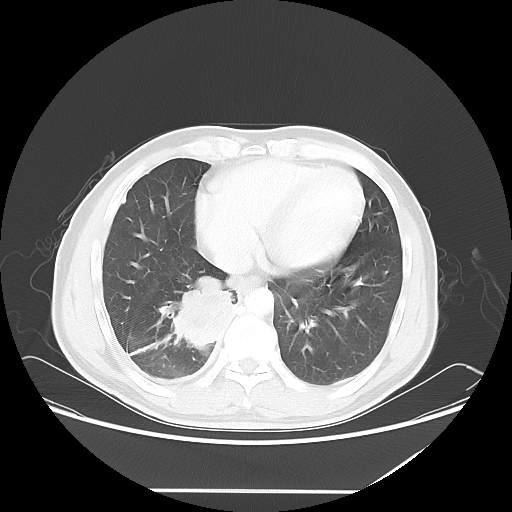
Chest CT, one axial slice; slice 21 of 60 in the series (ordered by position); reconstruction kernel LUNG; lung window (W 1500 / L -600 HU); 512 × 512 image matrix, field of view 419 × 419 mm. Patient: male, 48 years. From the clinical record (not read from this slice): clinical TNM (as recorded): T3 N3 M1a.
Annotated regions visible in this slice (bounding box drawn by a radiologist):
- lung tumour (recorded histology: squamous cell carcinoma): bounding box [x1, y1, x2, y2] px = [169, 275, 238, 355]